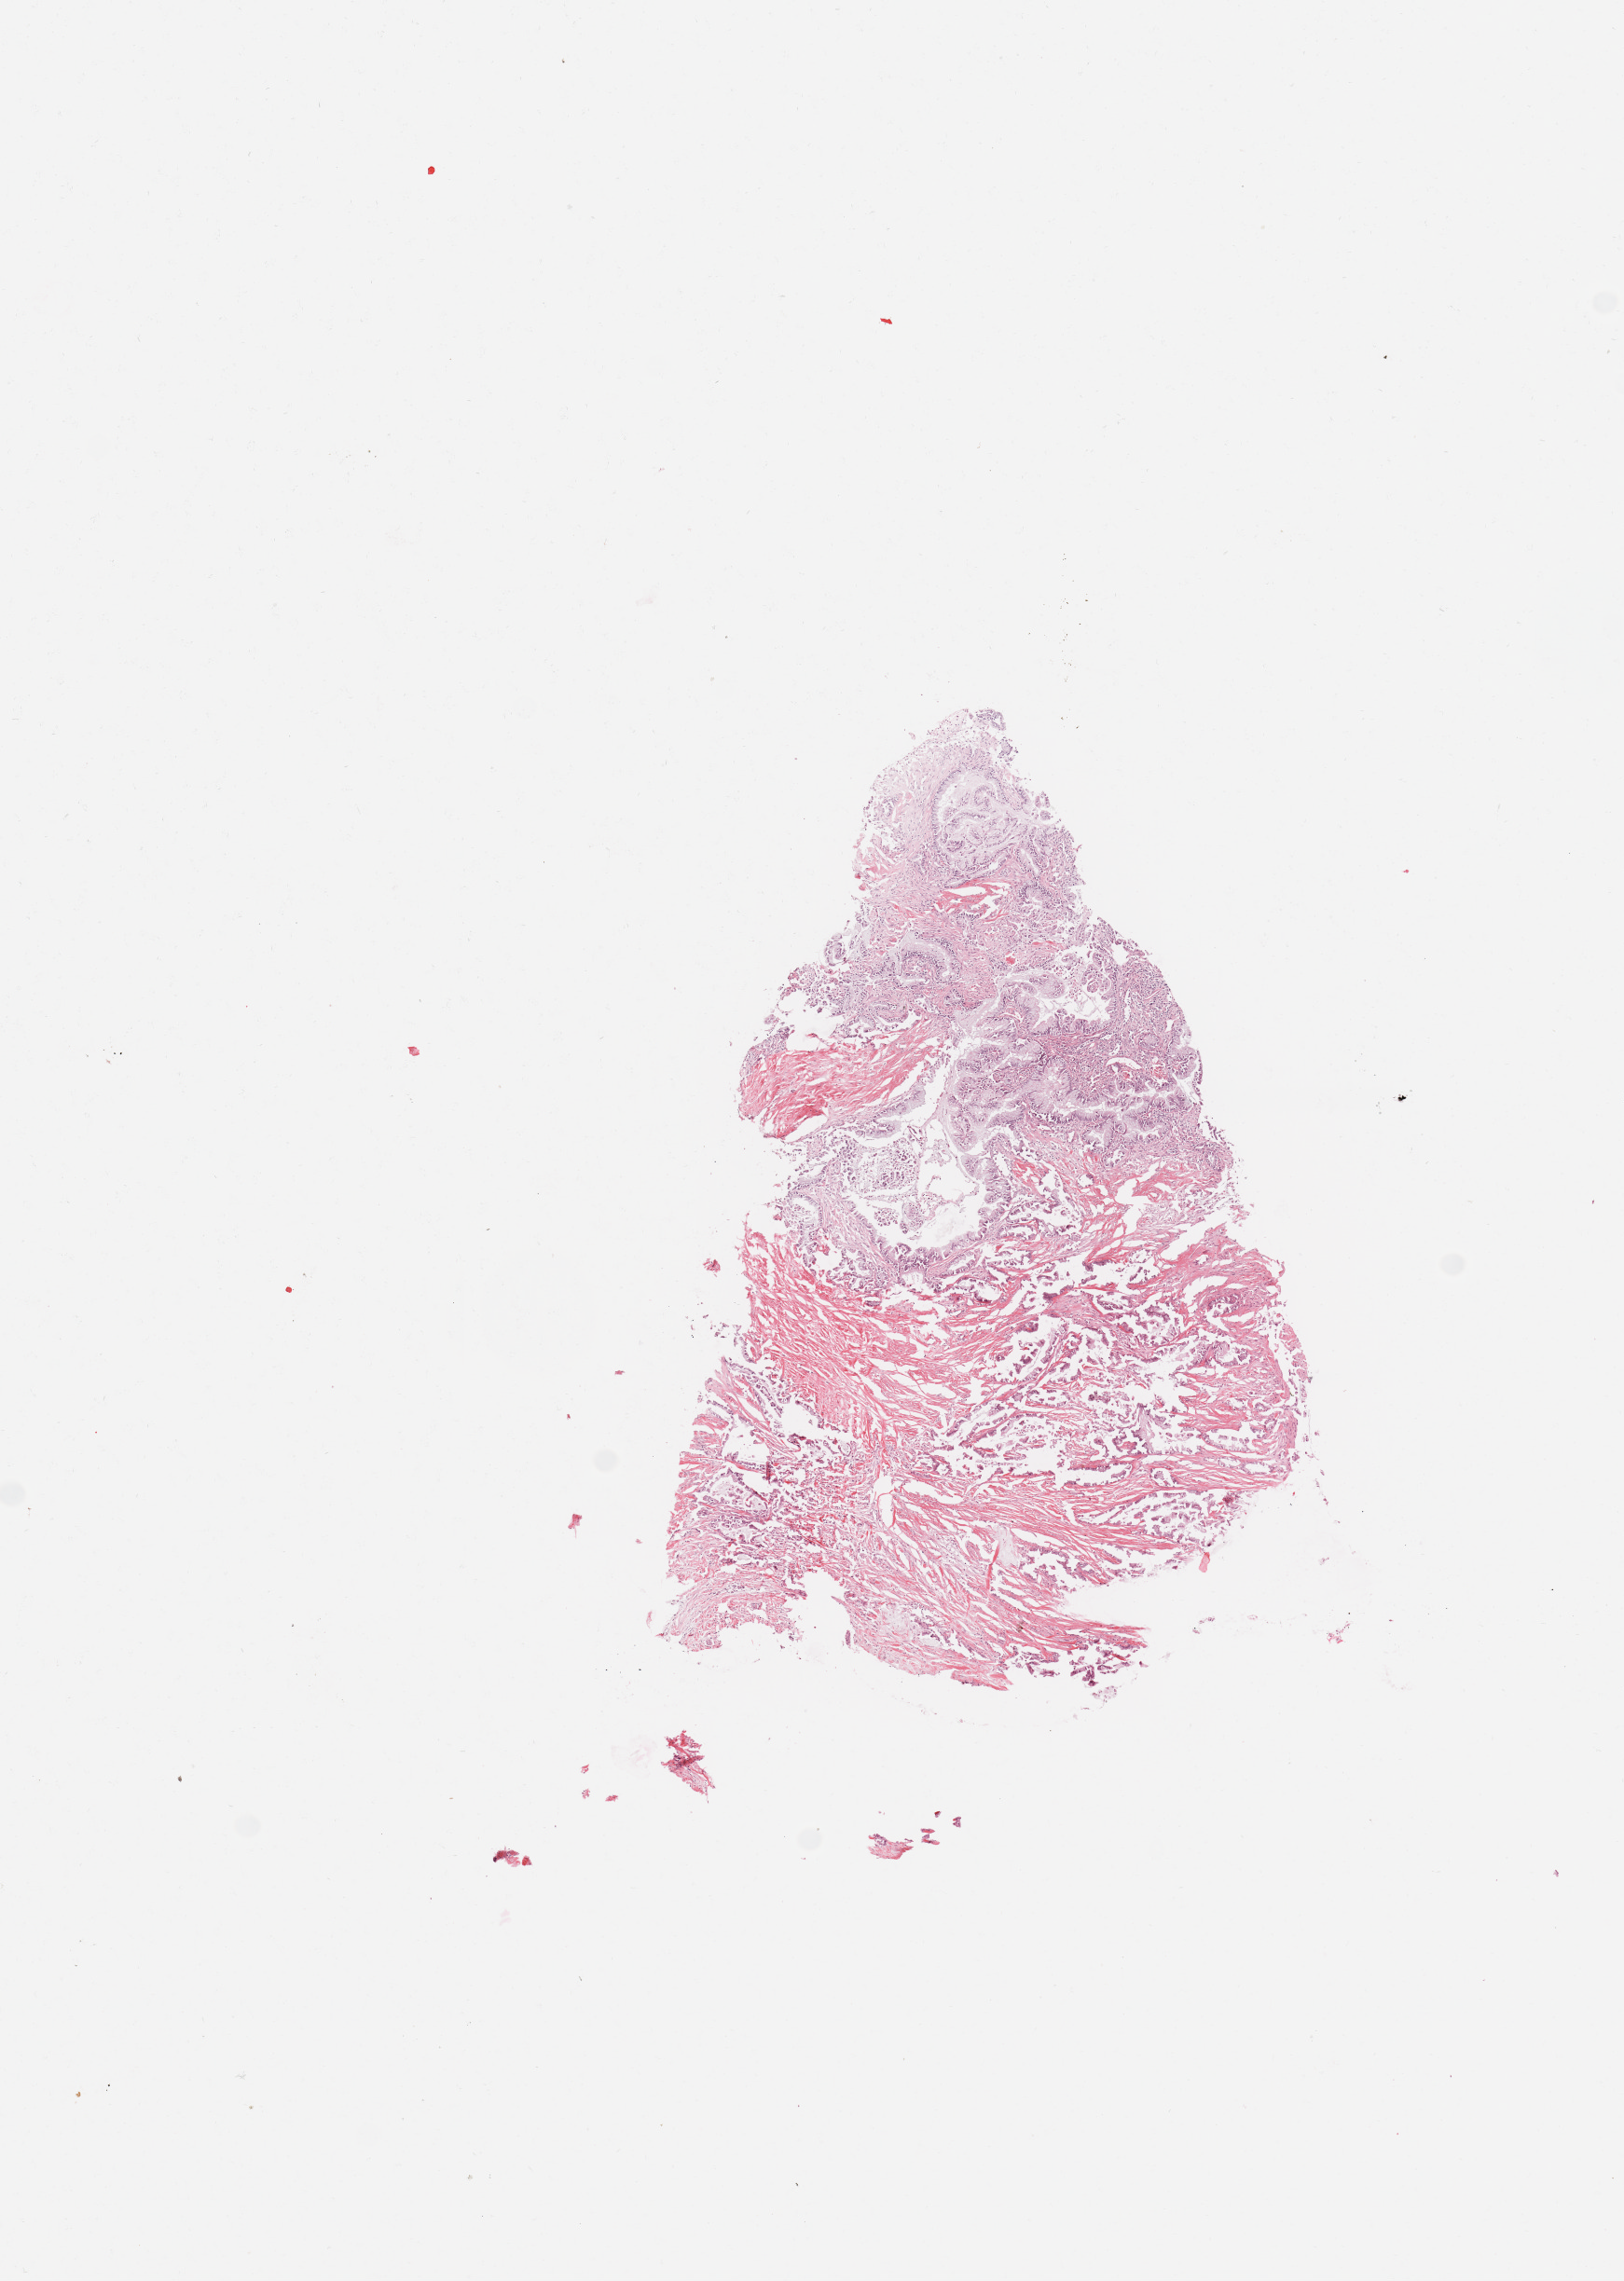
Hematoxylin and eosin (H&E) stained whole-slide image, a low-resolution overview of the entire scanned area, about 6.9 x 9.7 mm (slide scanned at 20x), tumour tissue sample, sampled site: pancreas. 54-year-old female patient. Pathologist review of this section (percent, as recorded): tumour nuclei 30%, necrosis 0%.
Histologic diagnosis: Infiltrating duct carcinoma, NOS.